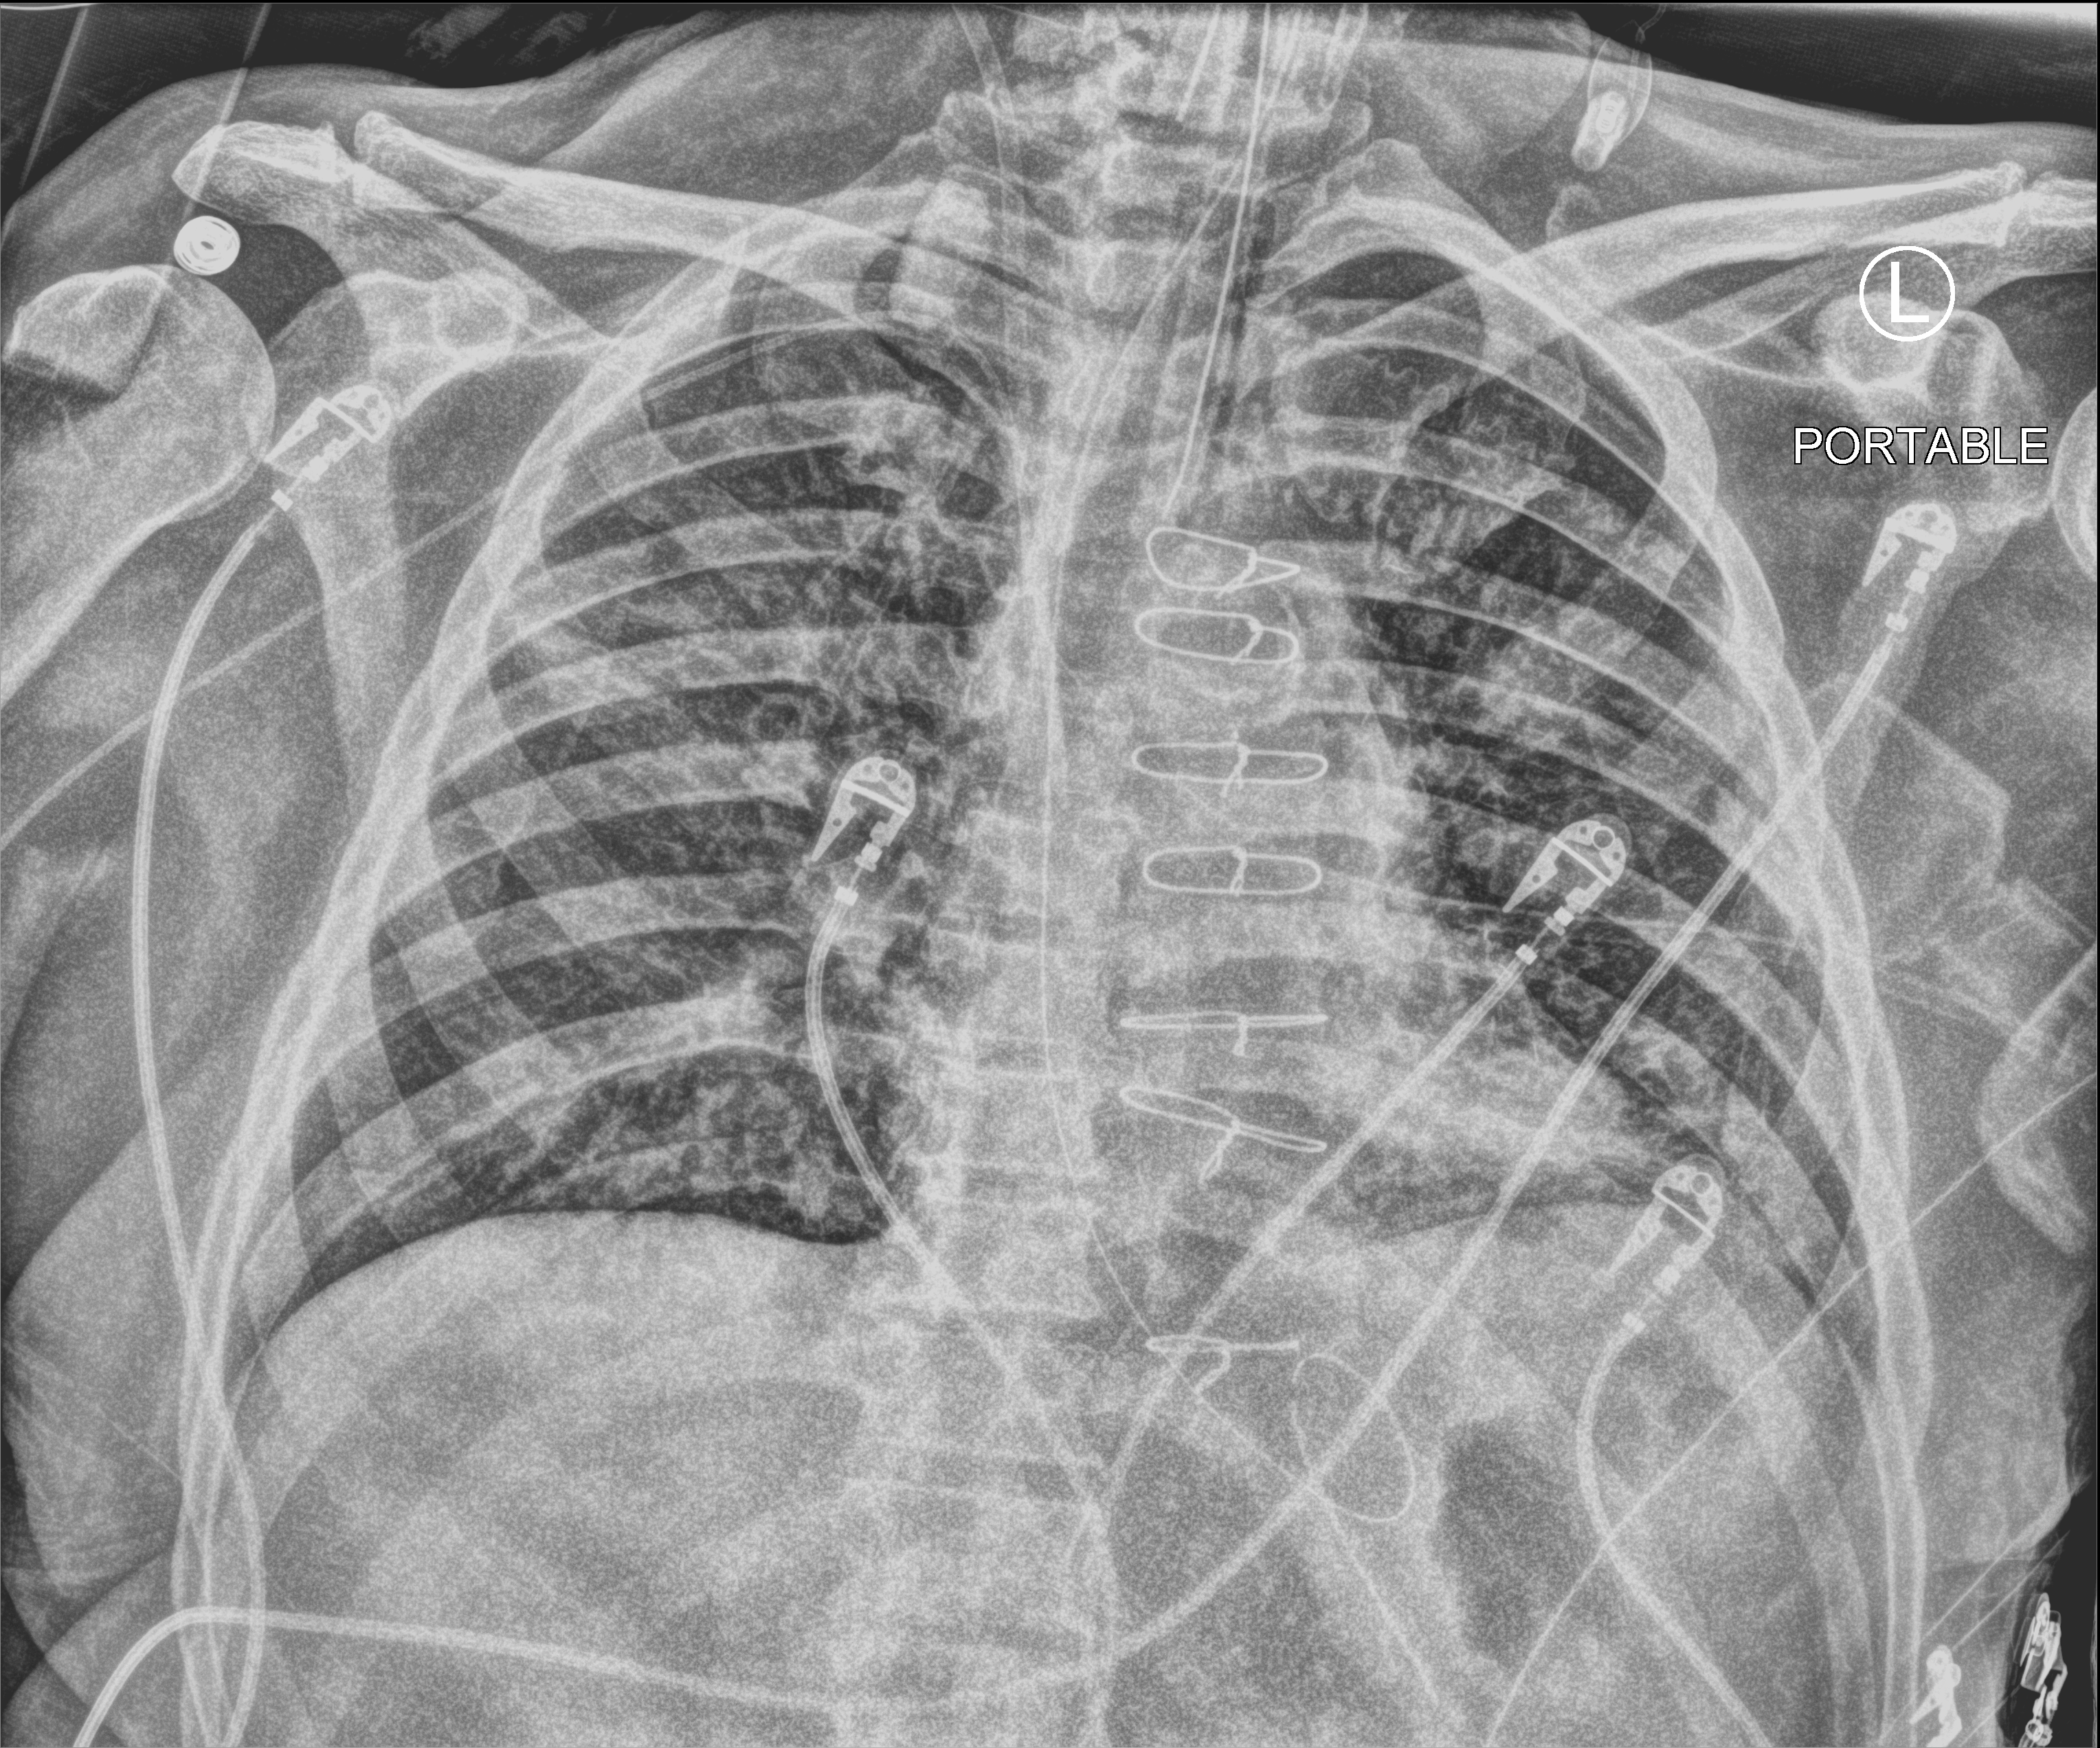
Bedside chest radiograph (computed radiography); anteroposterior (AP) projection. Patient hospitalised with COVID-19; male, aged 60–74 years.
Admission-level facts for this patient (not findings on this image; timing relative to this image not recorded):
- mechanically ventilated during this hospital stay: yes
- smoking status (admission record): former
- admitted to intensive care during this hospital stay: yes